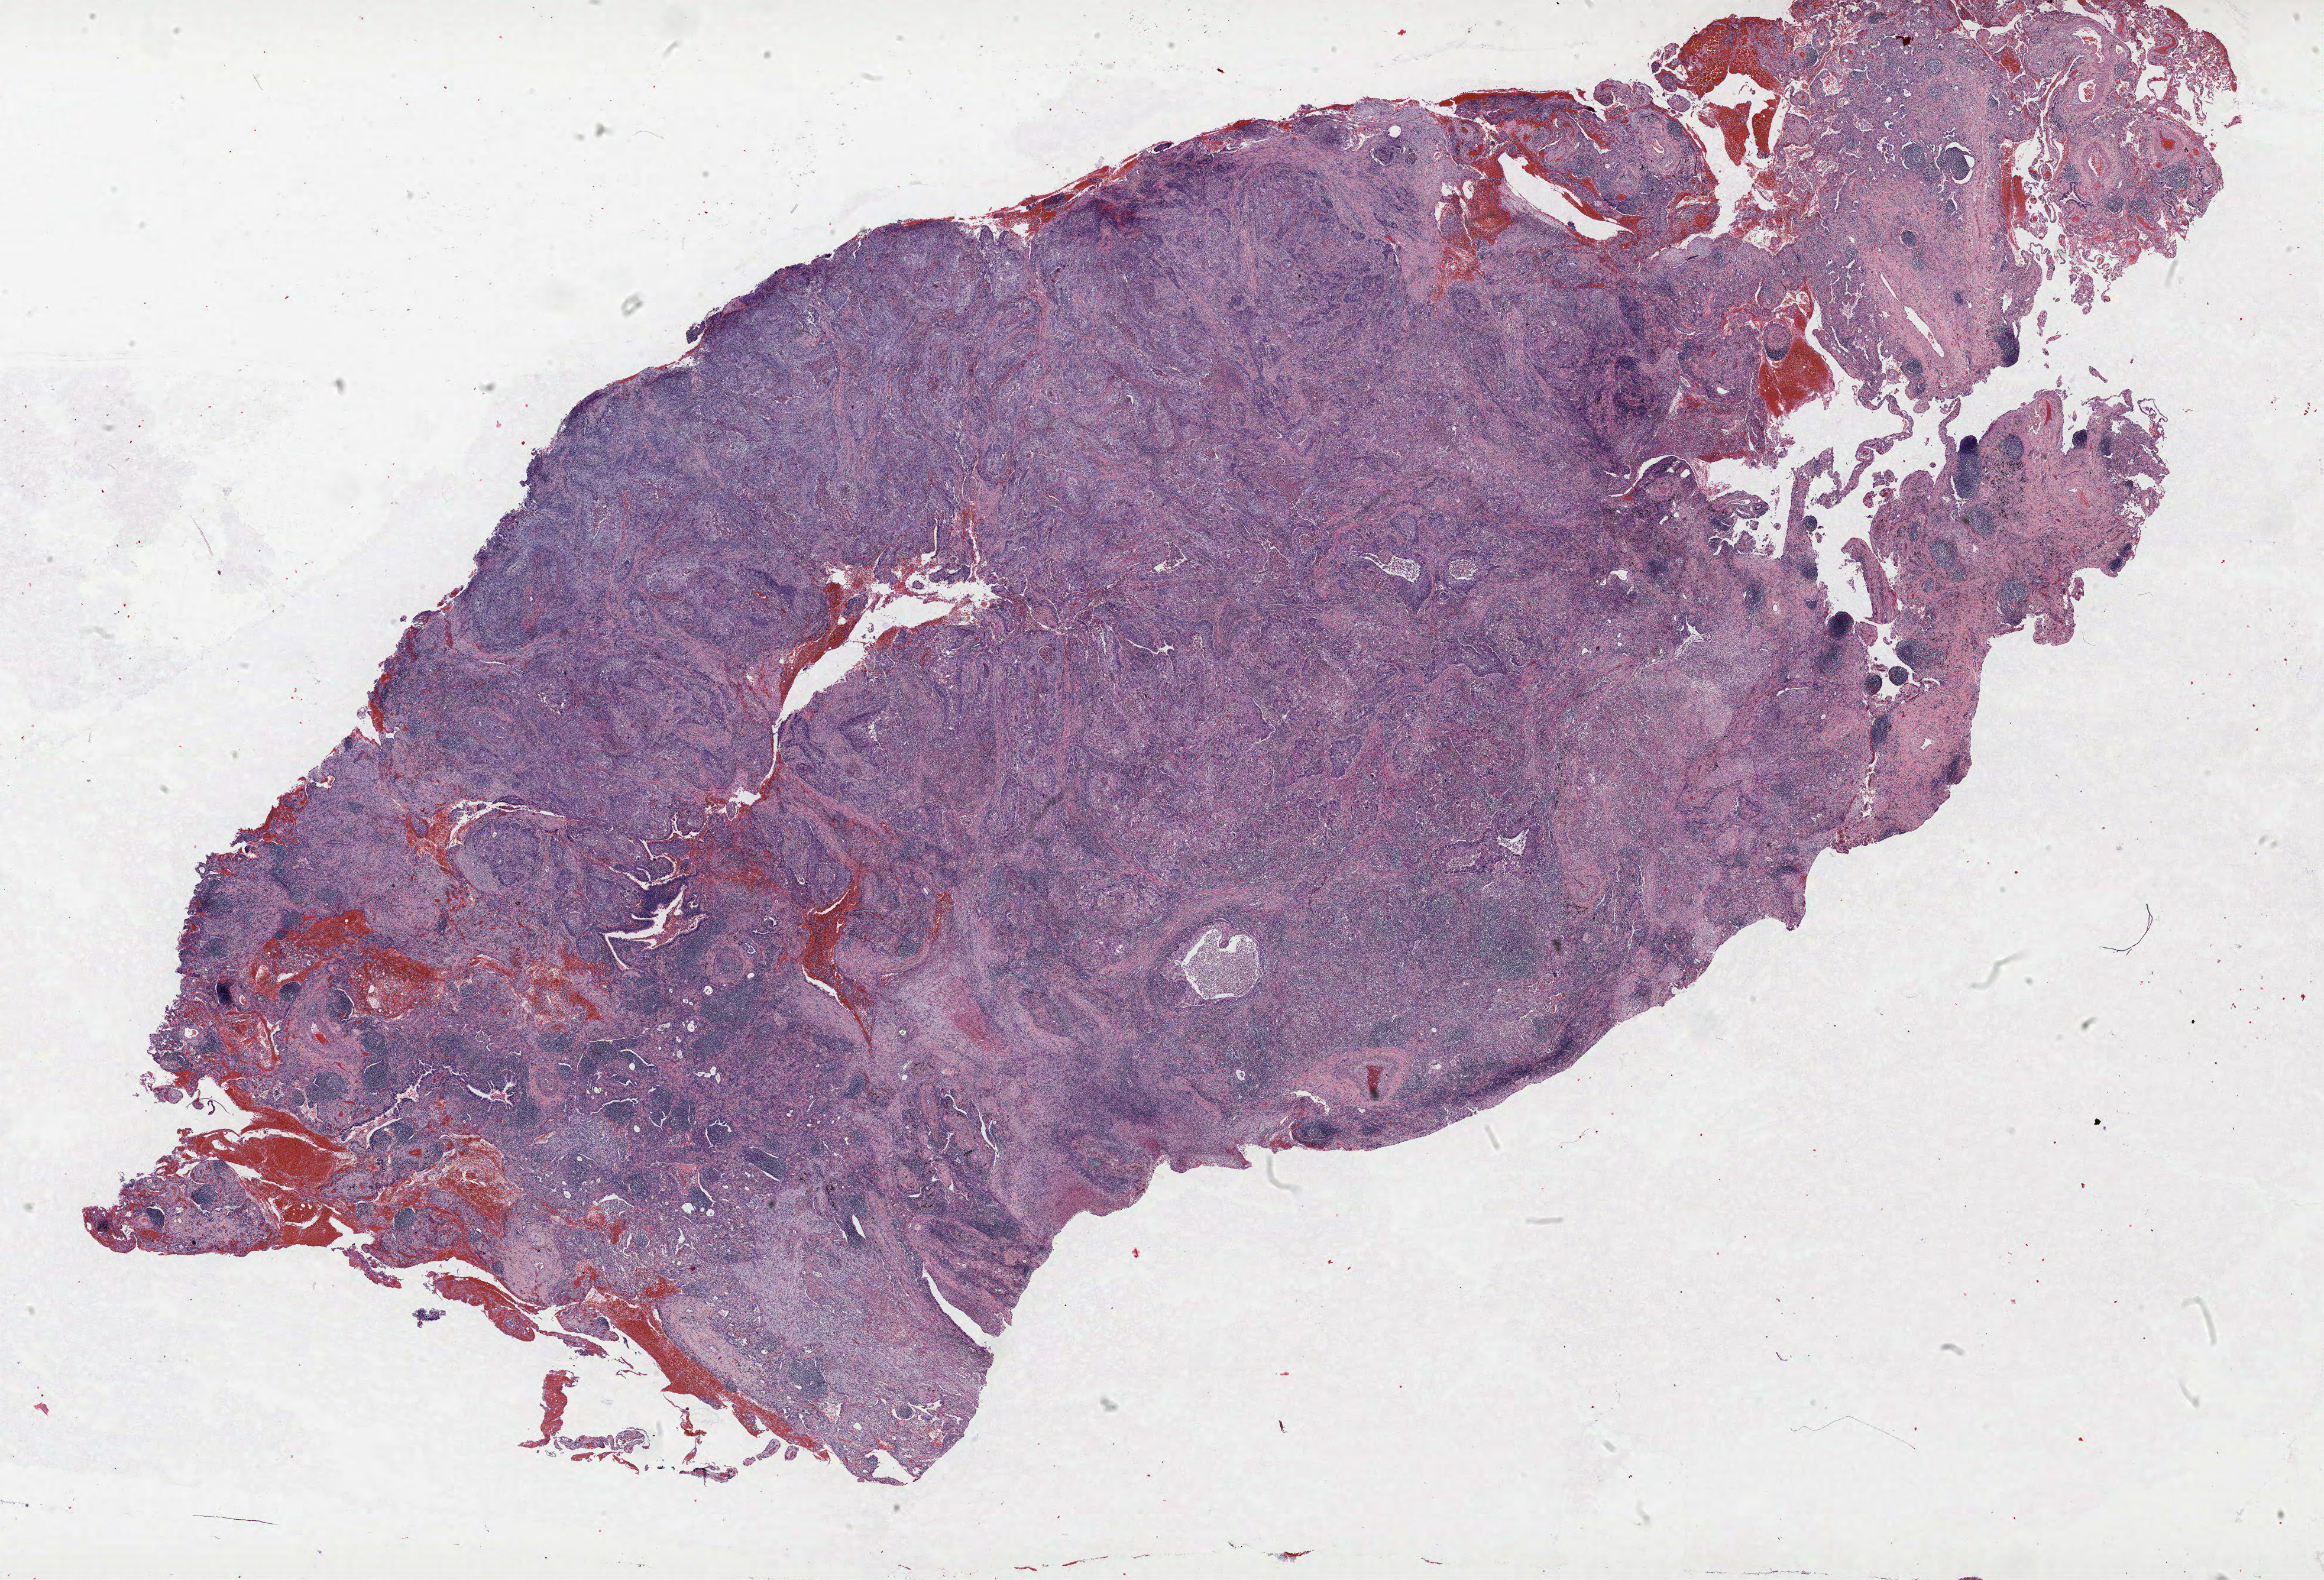
Whole-slide histology image, H&E — shown as a low-resolution overview of the whole scanned area (about 31.4 x 21.4 mm). FFPE section. Lung tissue. Male, age 72 at enrolment. Former smoker at enrolment. Grade: poorly differentiated (G3).
Stage (AJCC 6th edition): IIB. Primary tumour location (clinical record): right upper lobe. Tumour size (pathology): 43 mm. Participant's lung-cancer diagnosis: Squamous cell carcinoma, NOS.